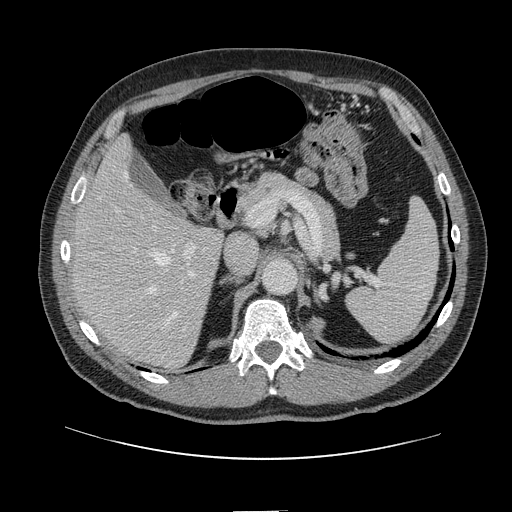
Contrast-enhanced abdominal CT, one axial slice. Slice 80 of 161 in the series (ordered by position). 120 kVp. Intravenous contrast given. Soft-tissue window (W 400 / L 40 HU). 2.5 mm slice thickness. 512 × 512 image matrix, field of view 412 × 412 mm. Male patient, age 66 years. From the clinical record (not read from this slice): diagnosis: colorectal cancer liver metastases, imaged before liver resection; multiple liver metastases: no; largest metastasis: 3.5 cm.
Structures marked on this image (expert manual segmentation):
- hepatic veins: box from (x=124, y=172) to (x=178, y=325) px
- liver: (x=75, y=139)–(x=222, y=367)
- planned liver remnant (the part of the liver to remain after resection): (x=75, y=139)–(x=201, y=299)
- portal vein (with intrahepatic branches): (x=131, y=225)–(x=197, y=279)